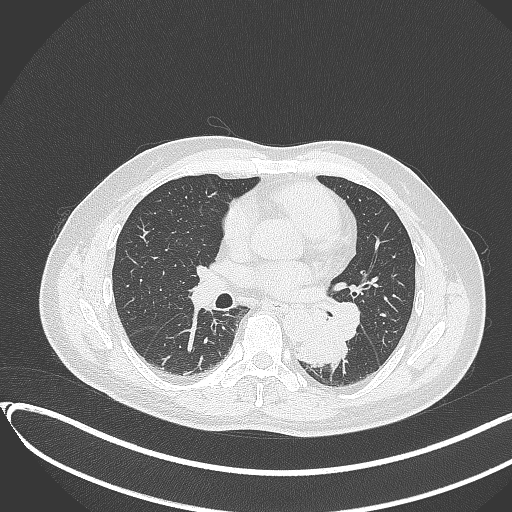
Chest CT, one axial slice. Slice 175 of 417 in the series (ordered by position). Reconstruction kernel B70f. 120 kVp. Lung window (W 1500 / L -600 HU). 512 × 512 image matrix, field of view 400 × 400 mm. Male patient, age 54 years. From the clinical record (not read from this slice): clinical TNM (as recorded): T3 N0 M0.
Outlined on this slice (rectangle marked by the reading radiologist):
- lung tumour (recorded histology: squamous cell carcinoma): bounding box (x1, y1, x2, y2) in pixels: (287, 321, 350, 376)